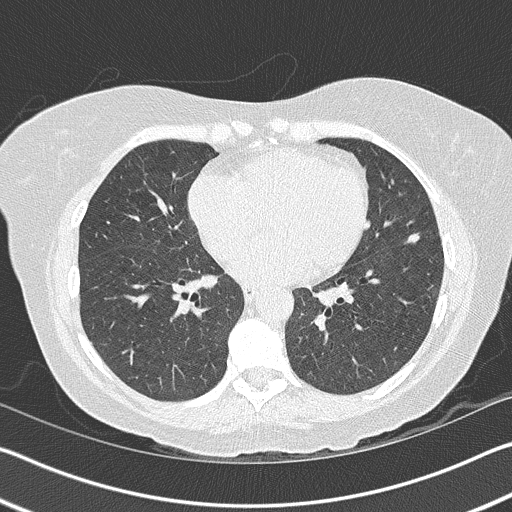
Axial slice from a low-dose chest CT screening exam, baseline screening round, lung window (W 1500 / L -600 HU), lung (sharp) reconstruction kernel (B50f), slice 70 of 157 in the series. Female participant, aged 63 years at enrolment. Current smoker at enrolment.
Lesion marked by an expert reader, bounding box (x1, y1, x2, y2) in pixels: (385, 218, 437, 258). The screening reader recorded 3 non-calcified nodules or masses ≥4 mm on this exam (right upper lobe, left upper lobe, lingula); which of them this box marks is not recorded. Official screen result: positive, change unspecified: nodule(s) >= 4 mm or enlarging nodule(s), mass(es), or other non-specific abnormalities suspicious for lung cancer.